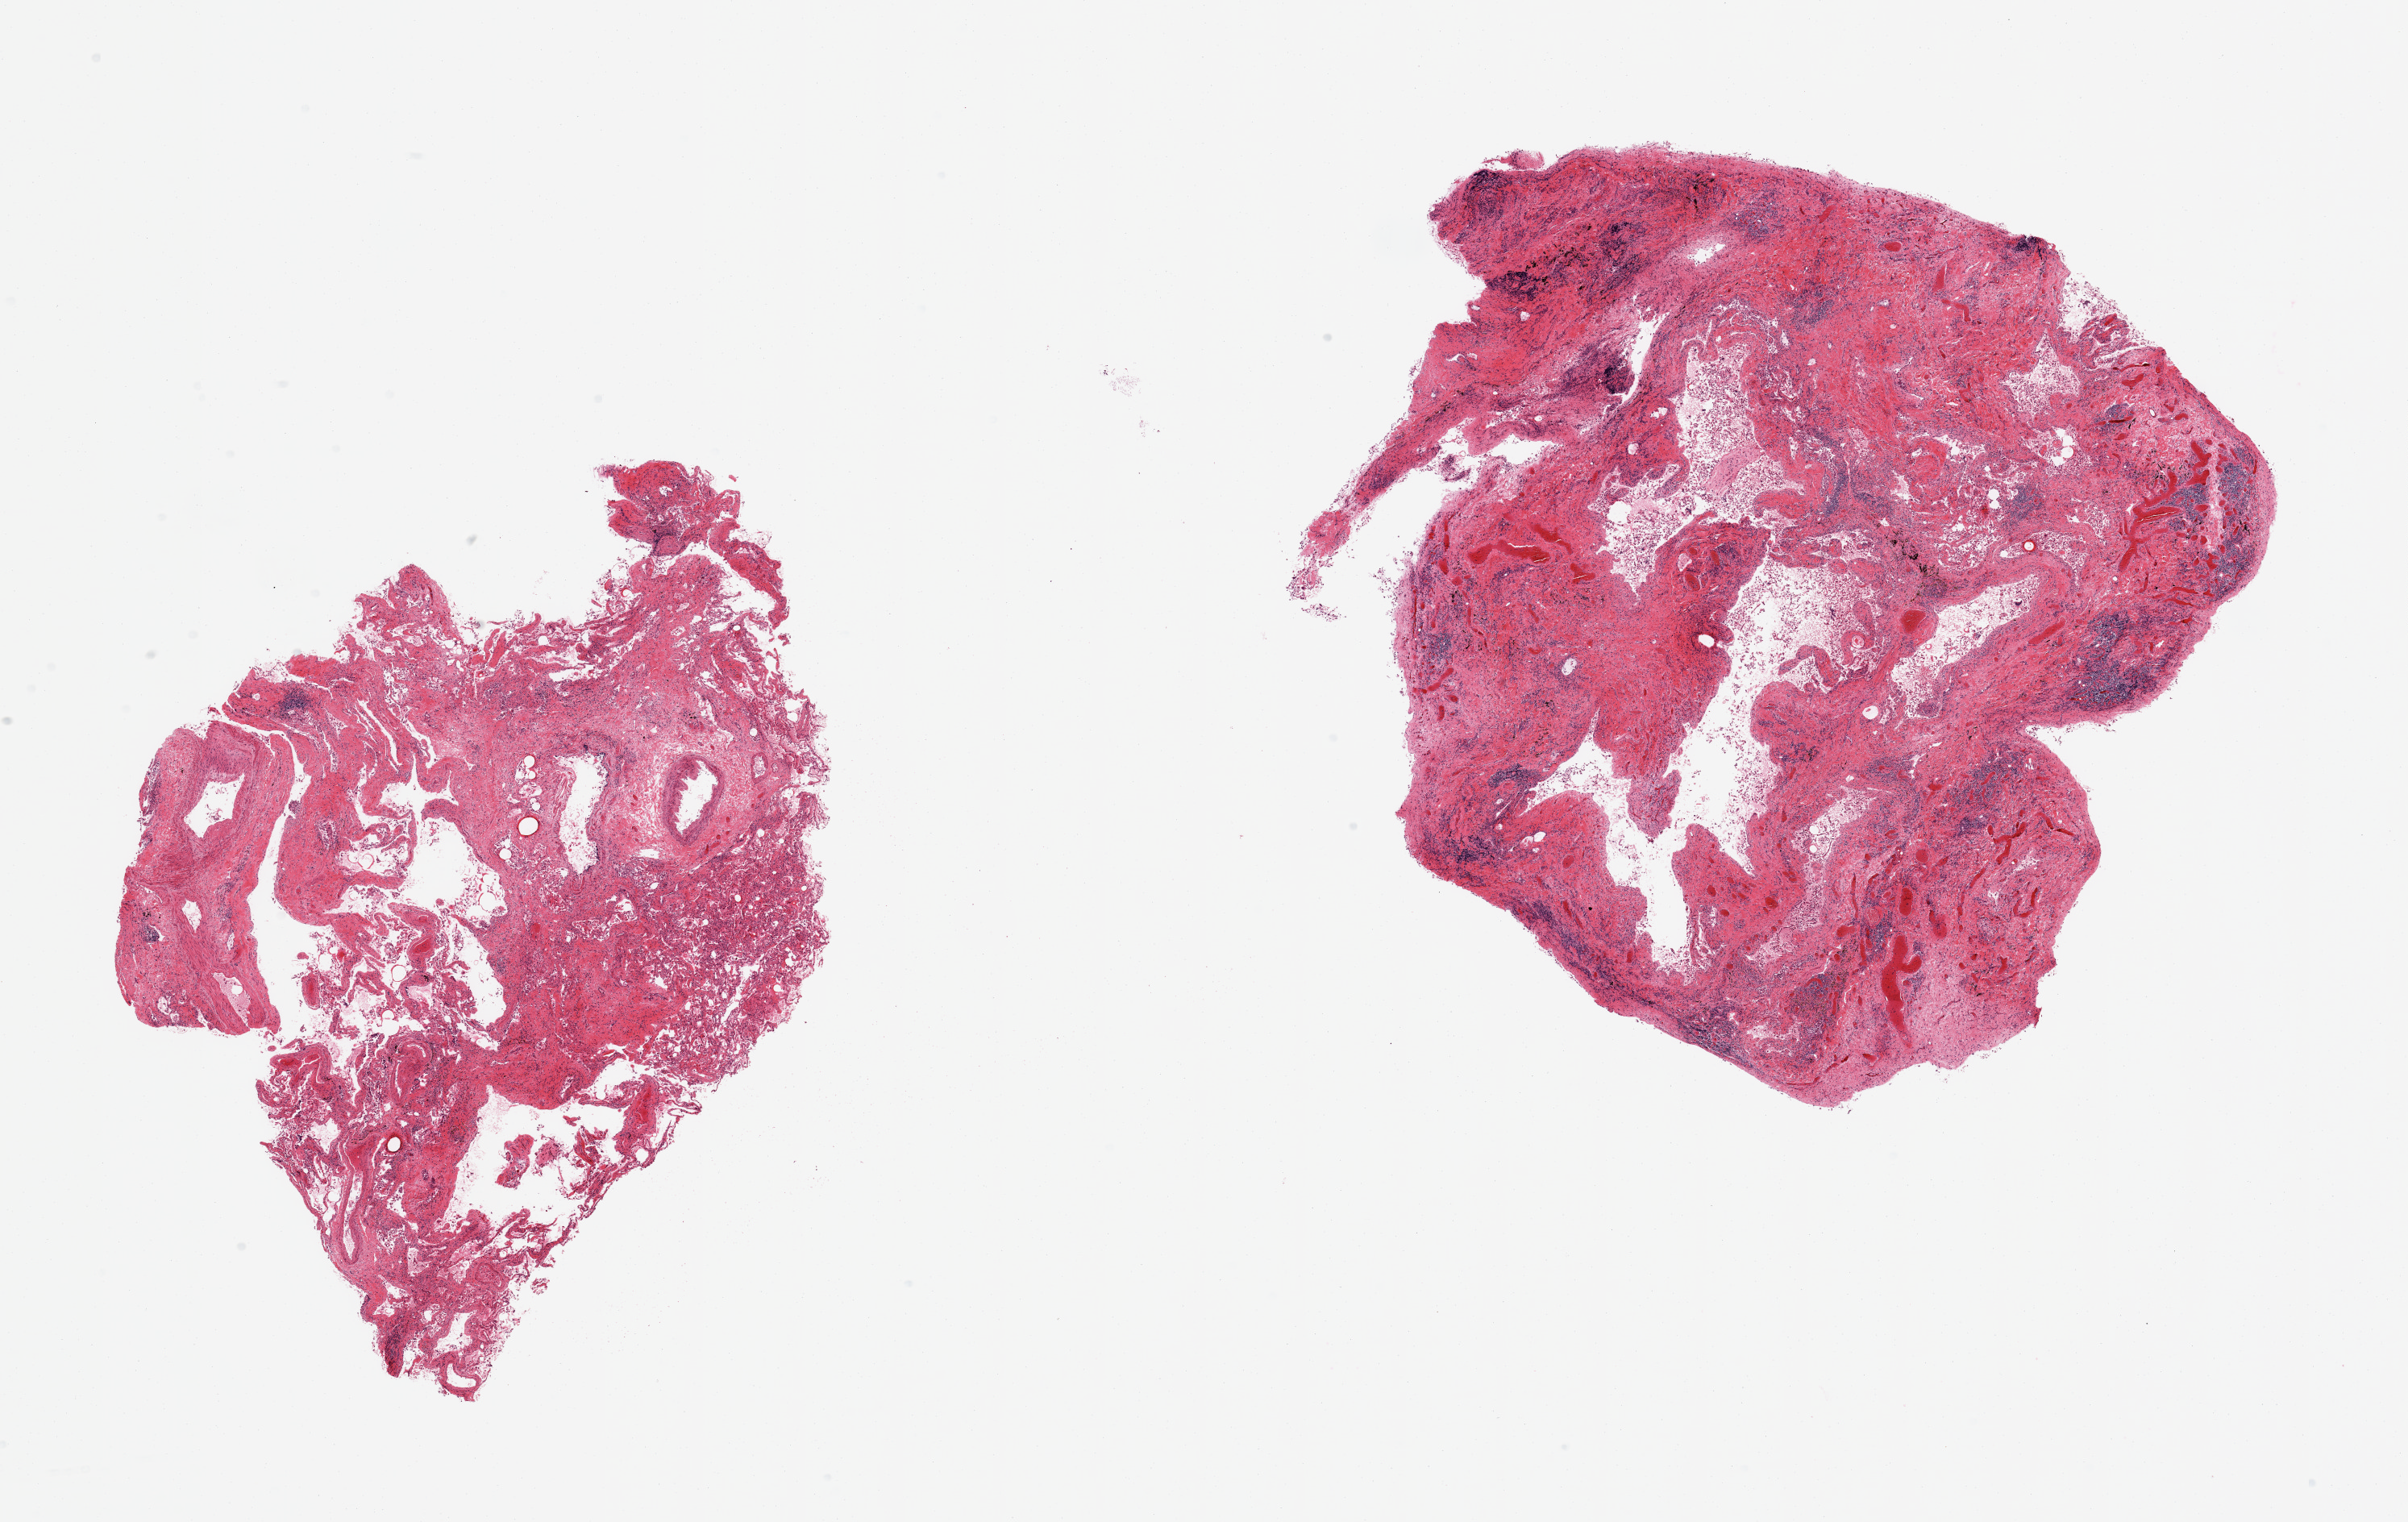
Digitized haematoxylin and eosin-stained section — low-resolution overview of the scanned area, about 23.6 x 14.9 mm. PAXgene-fixed, paraffin-embedded tissue. Sampled site (target tissue): lung. Tissue donor sample. Donor: male.
* reviewer comment on this tissue sample: 2 pieces; includes several large vessels, fibrosis and chronic inflammation with minimal normal lung tissue